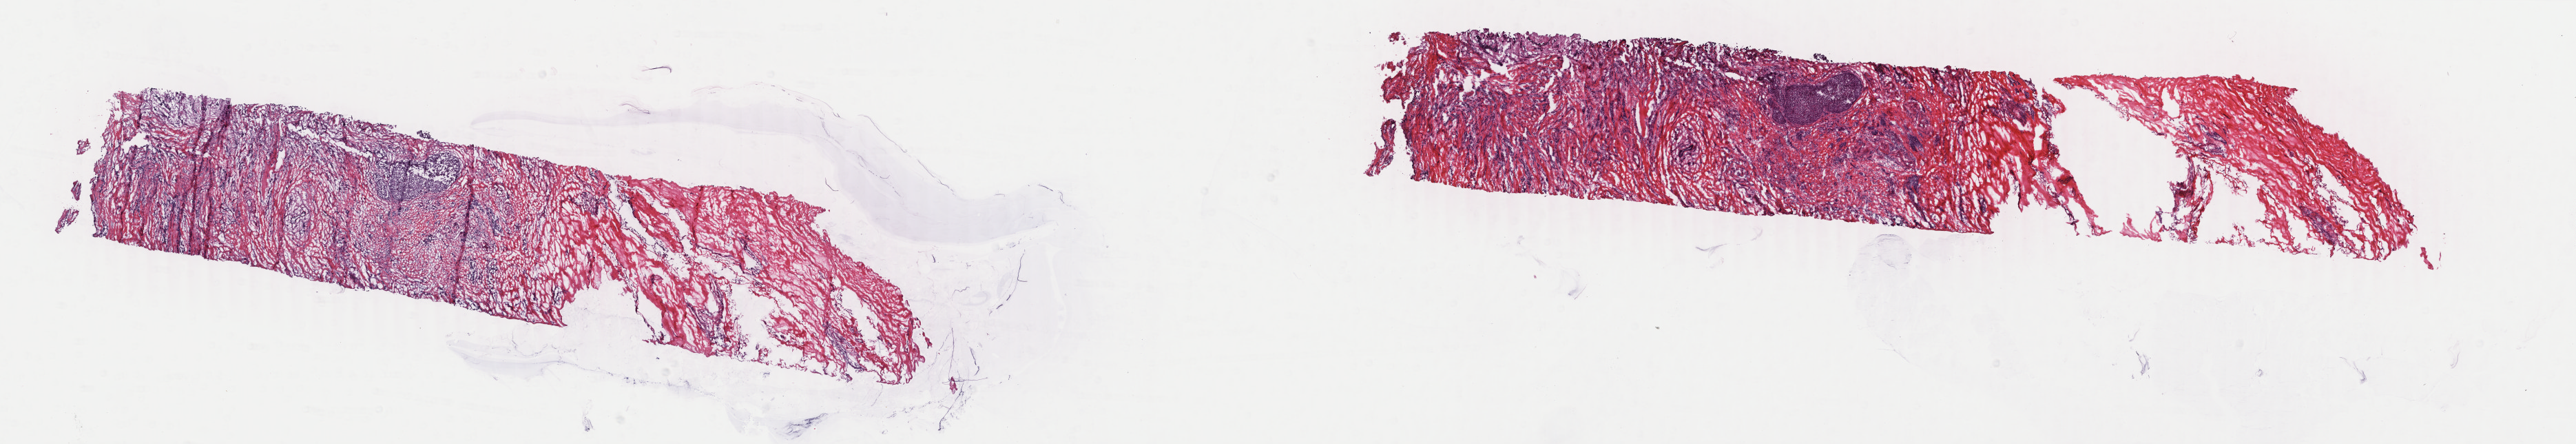
H&E whole-slide image — a low-resolution overview of the entire scanned area, about 29.7 x 5.1 mm. Frozen section from the top of the tissue portion. Sample: primary tumour, breast. Female, age 46 years at initial diagnosis. Pathologist review of this section (percent, as recorded): tumour cells 75%, tumour nuclei 75%, normal cells 3%, stromal cells 22%, necrosis 0%. Infiltration values recorded for this section: lymphocyte infiltration 2%, monocyte infiltration 0%, neutrophil infiltration 0%.
Lymph nodes positive (case pathology): 0 of 1 examined. AJCC pathologic stage: IIB. Histologic diagnosis: Lobular carcinoma, NOS.